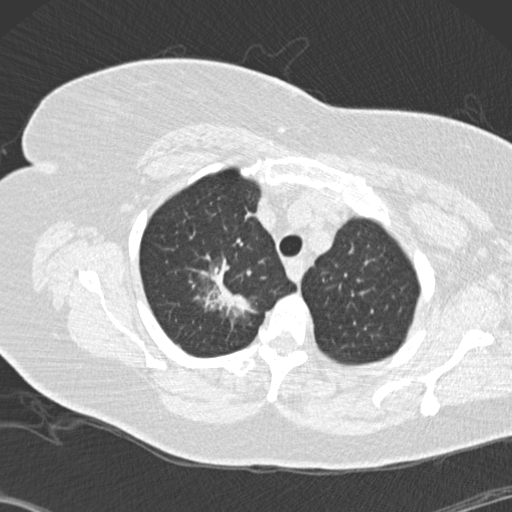
Low-dose screening chest CT, one axial slice; position 120 of 146 along the scan axis; reconstruction kernel B30f; lung window (W 1500 / L -600 HU); 2 mm slice thickness; 512 × 512 image matrix, field of view 350 × 350 mm.
Annotated regions visible in this slice (outlined manually by an expert reader):
- lesion 1 (tumor, upper lobe of right lung): bounding box [x1, y1, x2, y2] px = [201, 259, 255, 317]